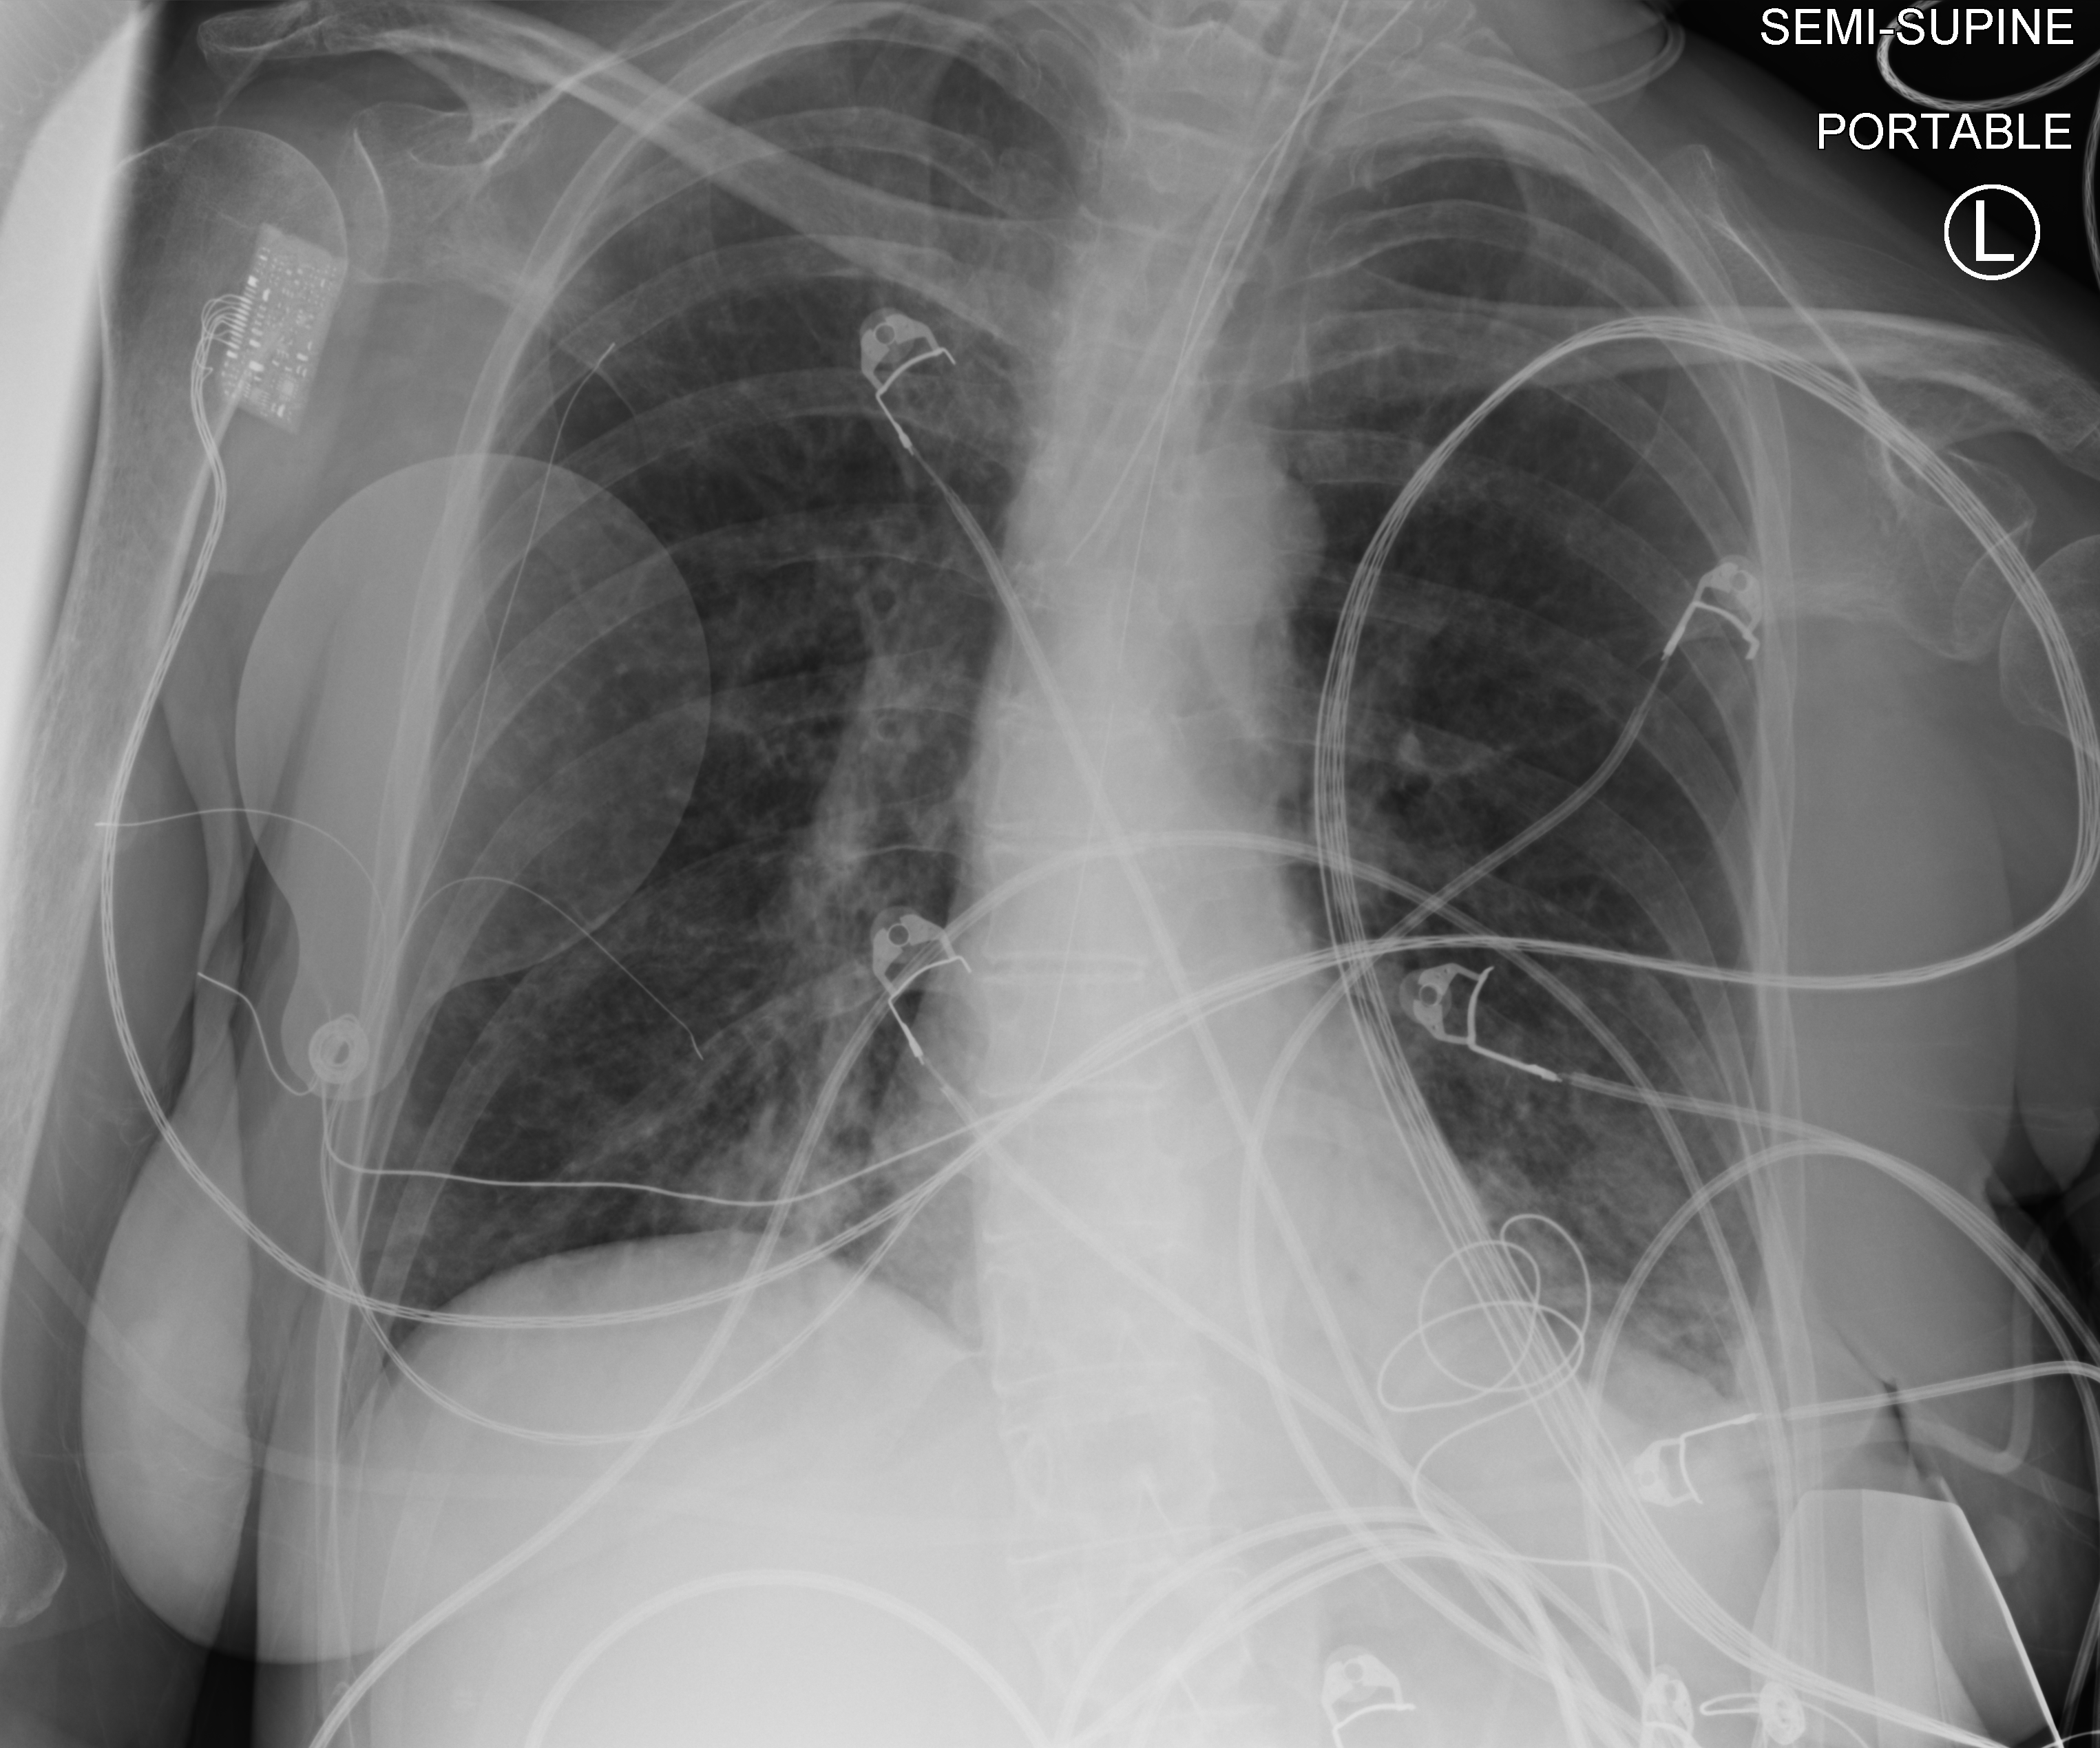
Portable chest radiograph, anteroposterior (AP) projection. Patient hospitalised with COVID-19, aged 18–59 years.
Admission-level facts for this patient (not findings on this image; timing relative to this image not recorded): admitted to intensive care during this hospital stay: yes; length of hospital stay: 11 days; mechanically ventilated during this hospital stay: yes.